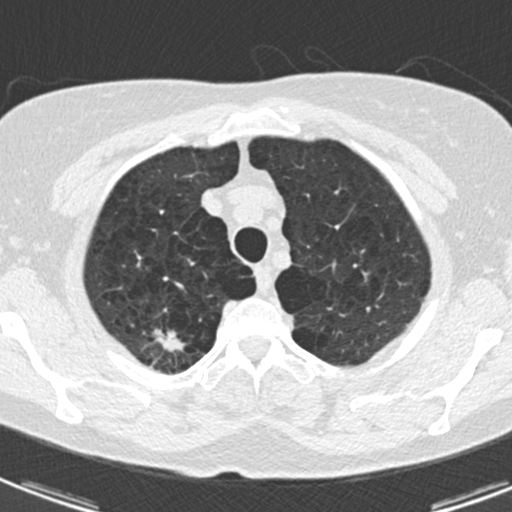
Axial slice from a low-dose chest CT screening exam. Third screening round (two years after baseline). Lung window (W 1500 / L -600 HU). 2 mm slice thickness. 512 × 512 image matrix, field of view 281 × 281 mm. Female, age 59 years at enrolment.
- Lesion marked by an expert reader, box from (x=133, y=320) to (x=193, y=366) px.
- Reader record for this screening exam (exam-level; its link to the box is not recorded): non-calcified nodule or mass ≥4 mm, right upper lobe, 12 × 7 mm, spiculated (stellate) margins, soft tissue attenuation, pre-existing on the prior screen: yes; interval growth: yes.
- Later outcome: lung cancer diagnosed 32 days after this screen — adenocarcinoma, NOS, right upper lobe, poorly differentiated (G3), stage IA (AJCC 6th edition), 20 mm at pathology.